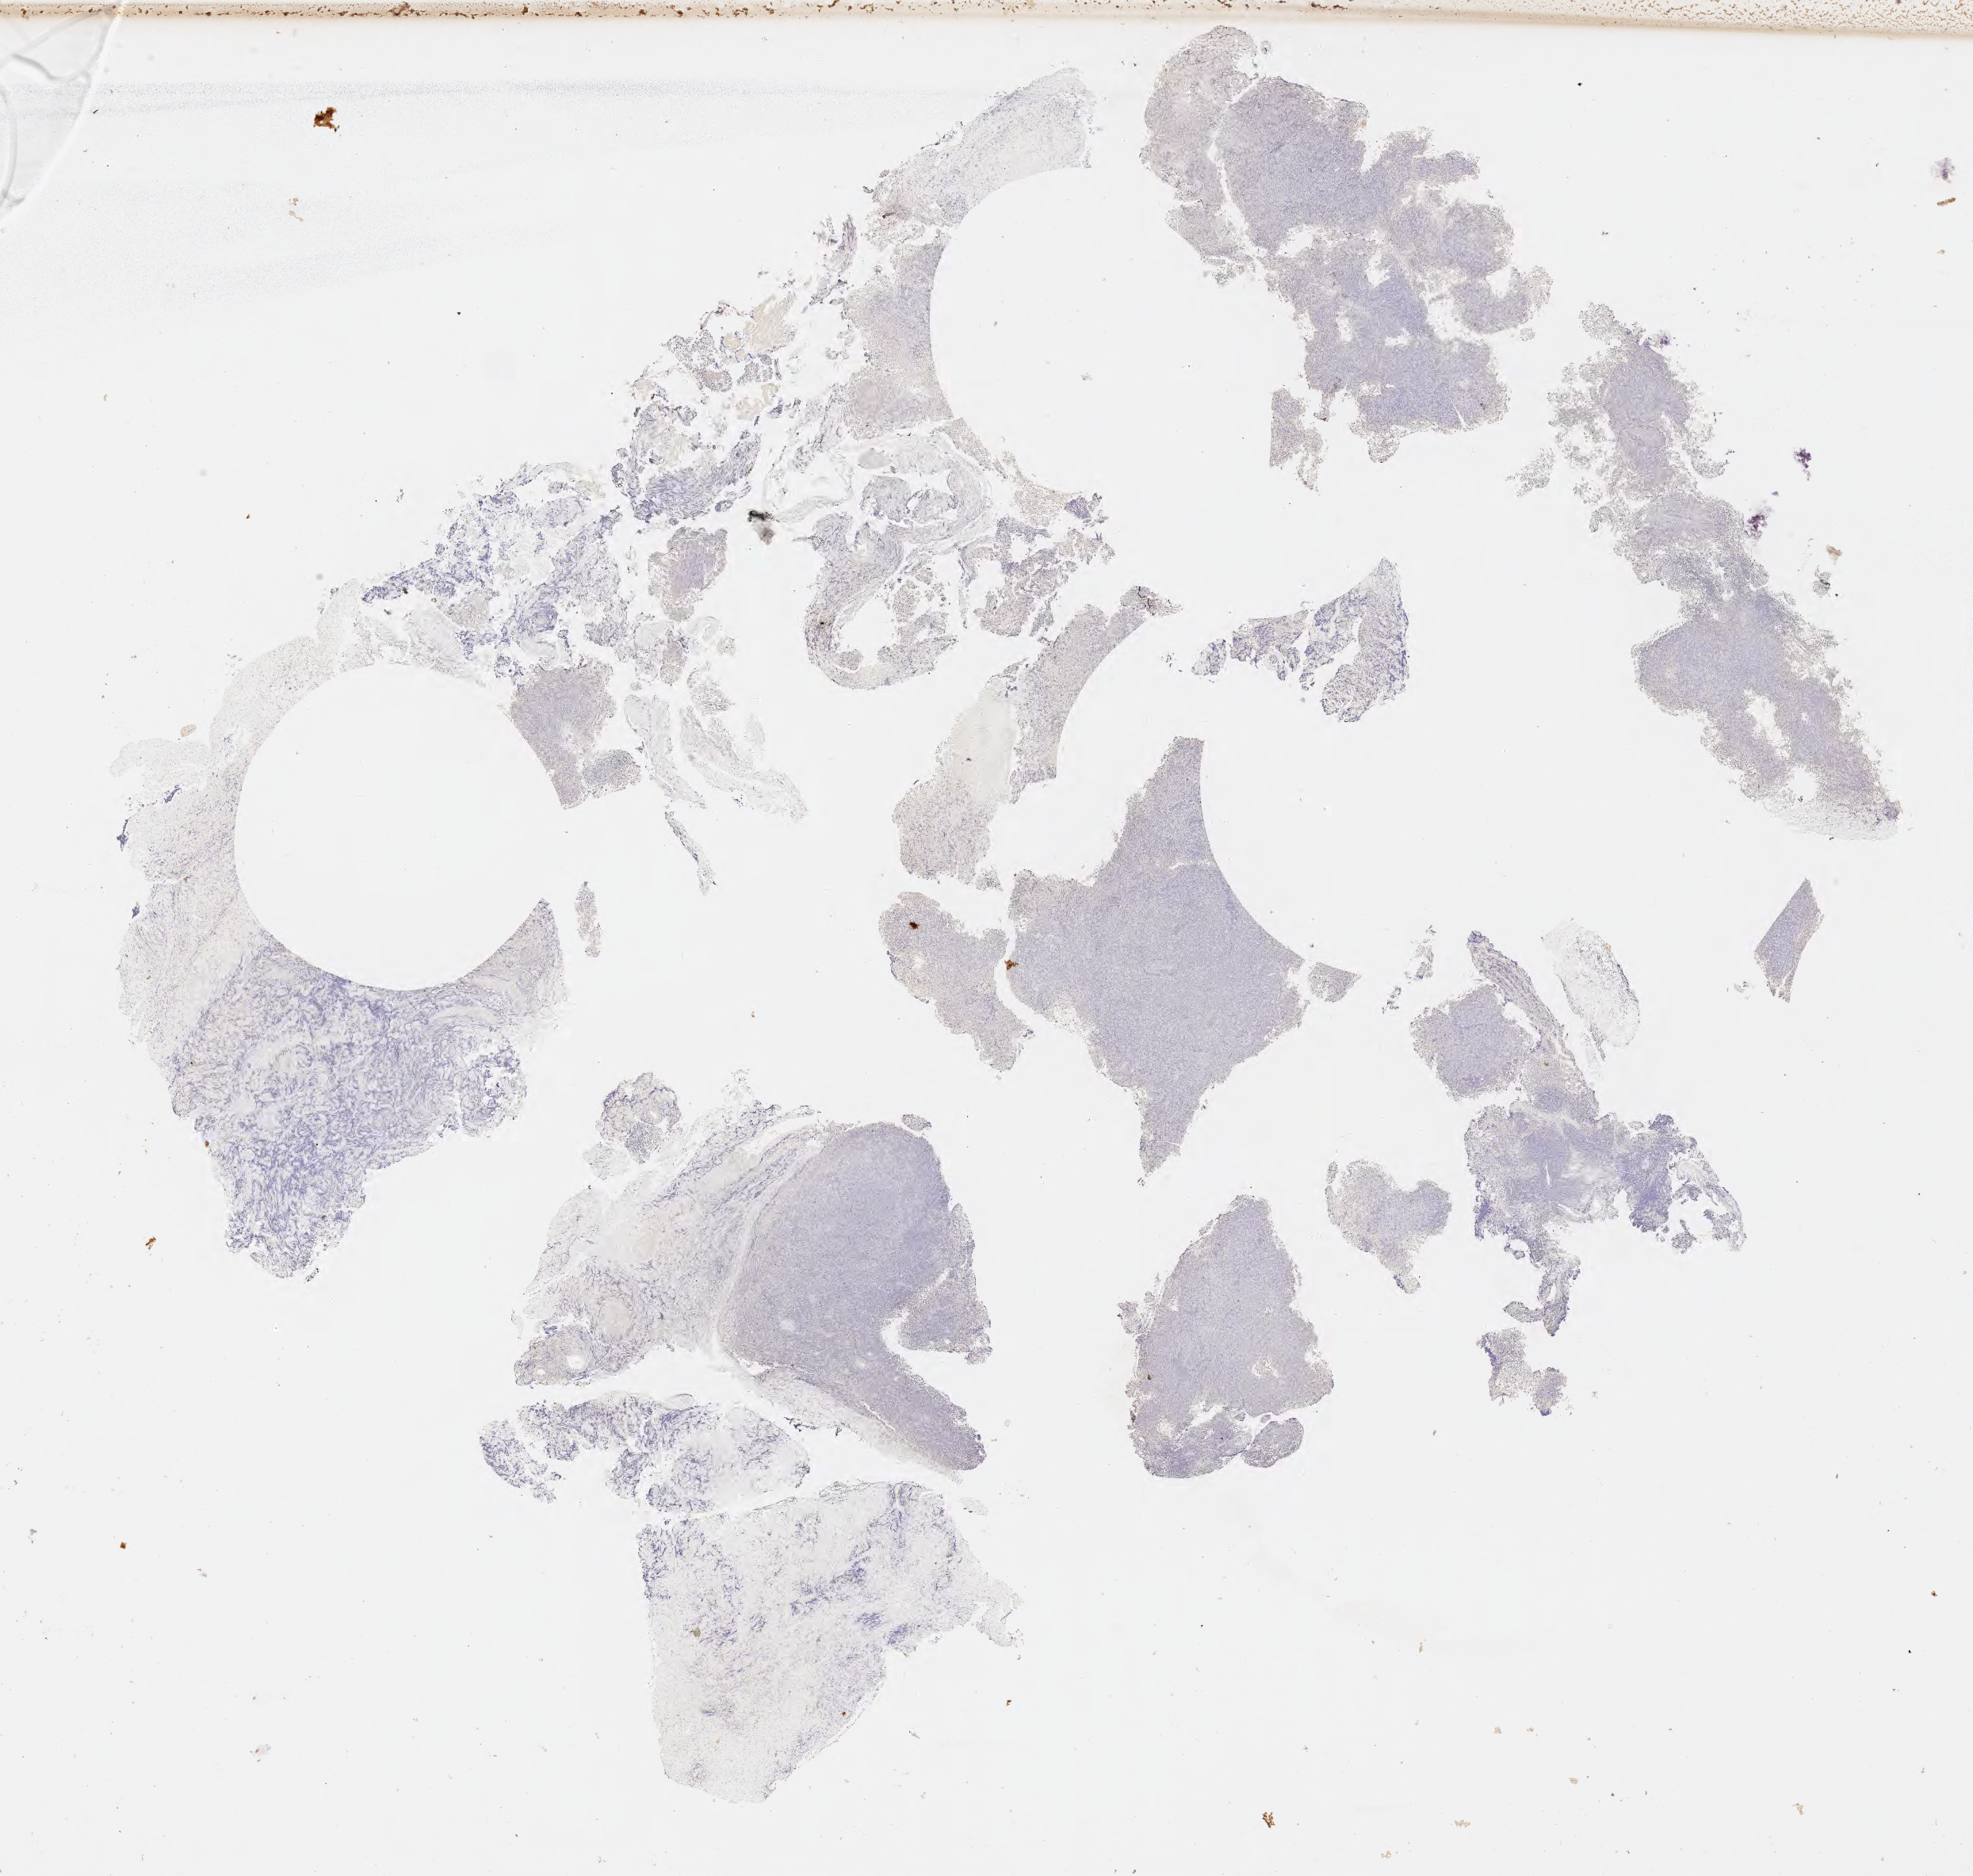
In-situ hybridisation whole-slide image, Epstein–Barr virus-encoded RNA (EBER) probe, a low-resolution overview of the entire scanned area, about 20.1 x 19.1 mm, specimen: tumor tissue, site: lymph node. Patient: male, 29 years old.
Diagnosis: Diffuse large B-cell lymphoma, NOS.